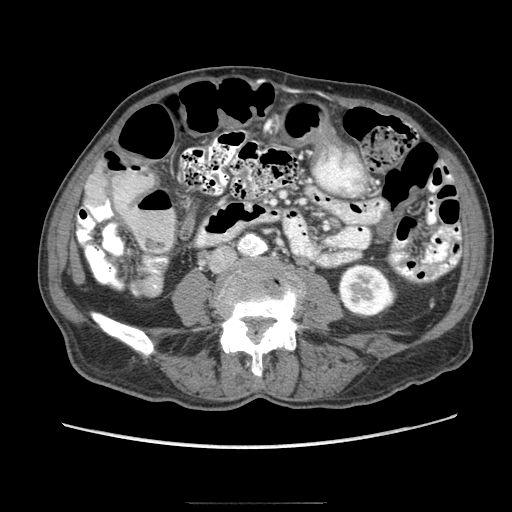
Contrast-enhanced abdominal CT (liver protocol), one axial slice; slice 8 of 83 in the series (ordered by position); reconstruction kernel STANDARD; 140 kVp; soft-tissue window (W 400 / L 40 HU); 512 × 512 image matrix, field of view 360 × 360 mm. From the clinical record (not read from this slice): diagnosis: hepatocellular carcinoma (patient treated with transarterial chemoembolisation; whether this scan precedes or follows treatment is not stated here); TNM stage (as recorded): Stage-I; Child-Pugh class: A; tumour differentiation: moderately differentiated; tumour nodularity: uninodular.
Outlined on this slice (semi-automatic segmentation, software-assisted and operator-edited):
- liver parenchyma outside the tumour (the mass and vessels are separate outlines, so this box may not span the whole liver): bounding box (x1, y1, x2, y2) in pixels: (84, 160, 107, 212)
- liver vessels: (86, 204, 97, 212)